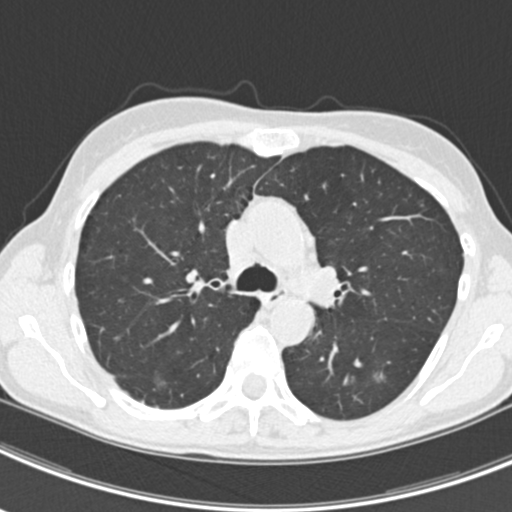
Chest CT (low-dose screening protocol), one axial image, second annual screen, lung window (W 1500 / L -600 HU), standard (soft-tissue) reconstruction kernel (B30f), 120 kVp. Female, age 63 years at enrolment. Current smoker at enrolment.
Expert-annotated lung lesion, bounding box [x1, y1, x2, y2] px = [365, 364, 398, 393]. The screening reader recorded 9 non-calcified nodules or masses ≥4 mm on this exam (left upper lobe, right upper lobe, left upper lobe, left lower lobe, right middle lobe, left lower lobe, left lower lobe, right lower lobe, right lower lobe); which of them this box marks is not recorded. Lung cancer was diagnosed 408 days after this screen (after the third annual screen): bronchiolo-alveolar adenocarcinoma, NOS, right upper lobe, right middle lobe, right lower lobe, left upper lobe, left lower lobe, moderately differentiated (G2), stage IV (AJCC 6th edition).